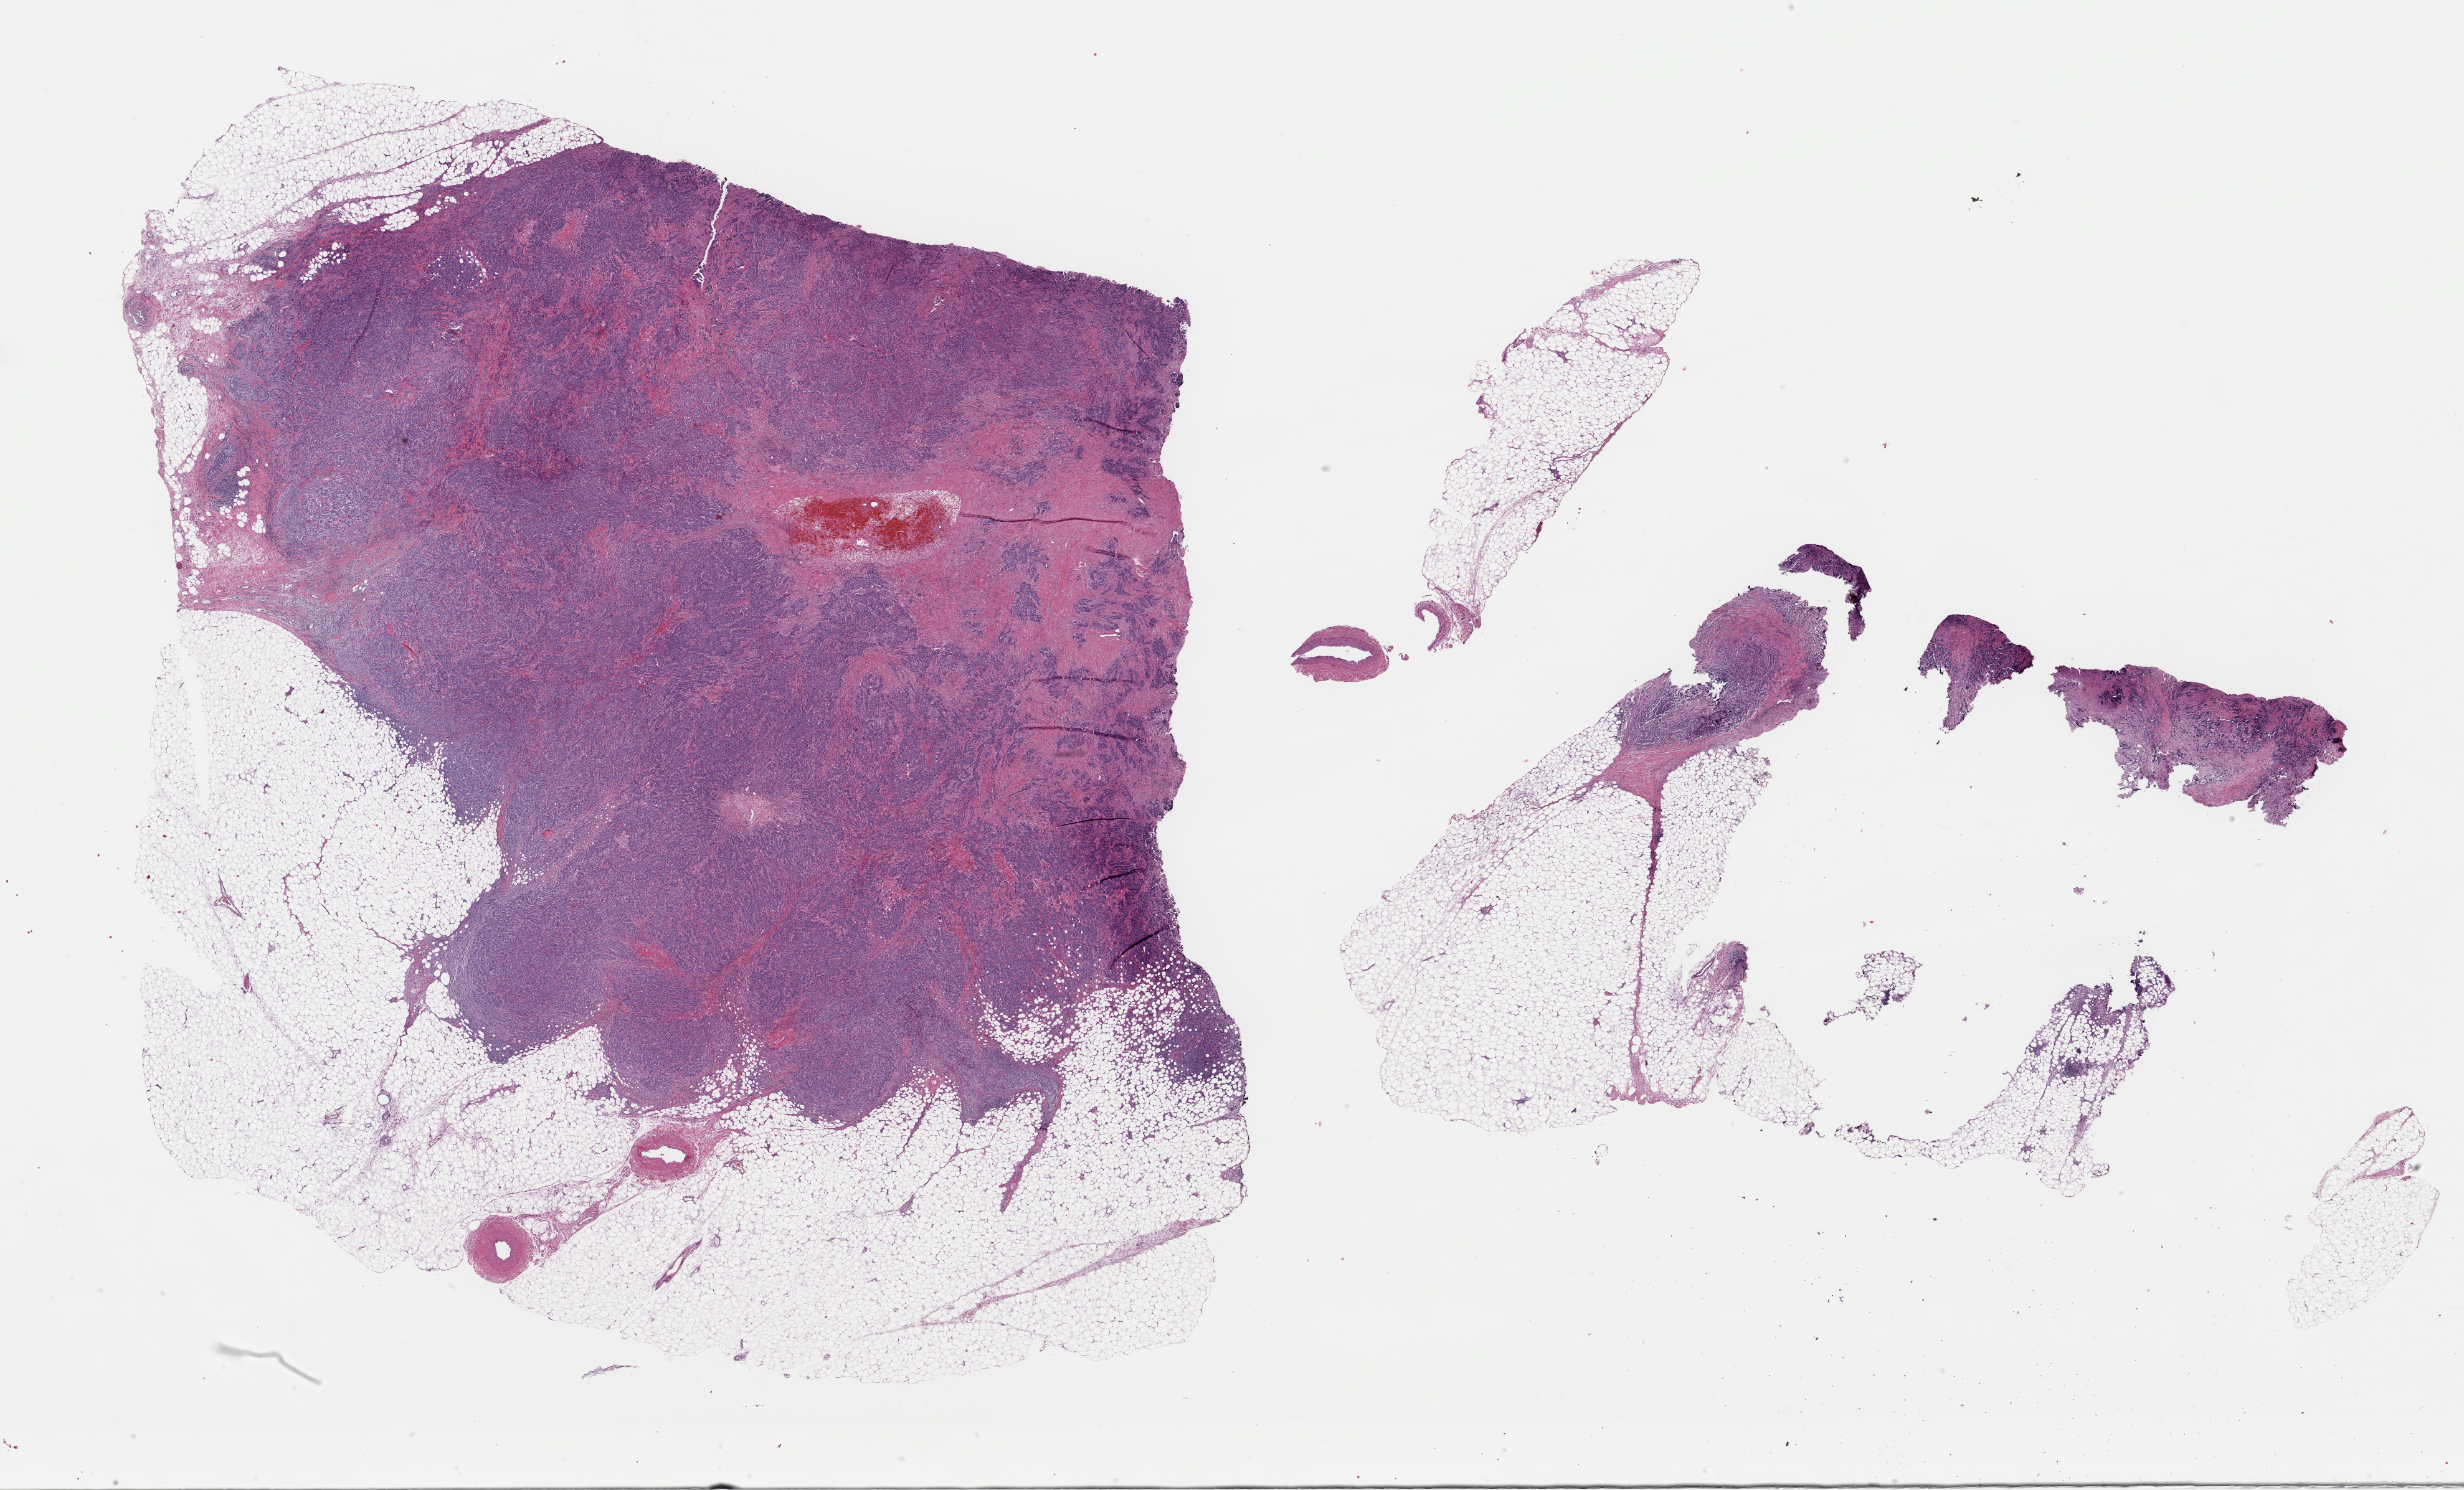
Digitized Hematoxylin and eosin (H&E) stained tissue section (whole slide) — a low-resolution overview of the entire scanned area, about 31.2 x 18.9 mm (from a 40x scan); formalin-fixed paraffin-embedded (FFPE) diagnostic section; sample: primary tumour, breast. Female patient; age at initial diagnosis 53 years.
* histologic diagnosis: Infiltrating duct carcinoma, NOS
* laterality: right
* AJCC pathologic stage: IIIA (6th edition)
* TNM: T2 N2 M0
* lymph nodes positive (case pathology): 5 of 19 examined